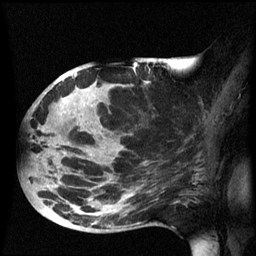
Breast MRI (dynamic contrast-enhanced), one sagittal slice. Dynamic contrast-enhanced series, image 2 of 3 at this slice position (ordered by acquisition). 1.5 T. TE 4.2 ms, TR 8.4 ms. 2.5 mm slice thickness. 256 × 256 image matrix. Patient: female, 49 years.
Annotated regions visible in this slice (semi-automatic segmentation, software-assisted and operator-edited):
- analysis volume of interest (the breast-tissue region the enhancement analysis was run in; not a lesion): bounding box <24,72,168,233> (left, top, right, bottom; pixels)
- tumour enhancement mask (voxels above the 70 % enhancement threshold inside the analysis volume of interest): <75,74,77,77>